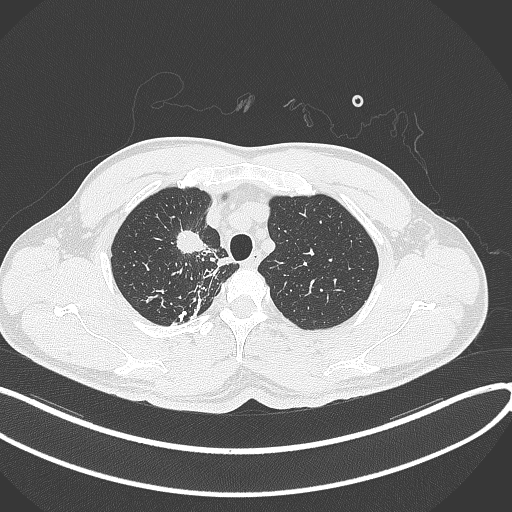
Chest CT, one axial slice. Slice 311 of 391 in the series (ordered by position). Reconstruction kernel B70f. 120 kVp. Lung window (W 1500 / L -600 HU). 512 × 512 image matrix, field of view 400 × 400 mm. Patient: male, 48 years. From the clinical record (not read from this slice): clinical TNM (as recorded): T1c N1 M1.
Annotated regions visible in this slice (rectangle marked by the reading radiologist):
- lung tumour (recorded histology: adenocarcinoma): bounding box <172,224,214,264> (left, top, right, bottom; pixels)